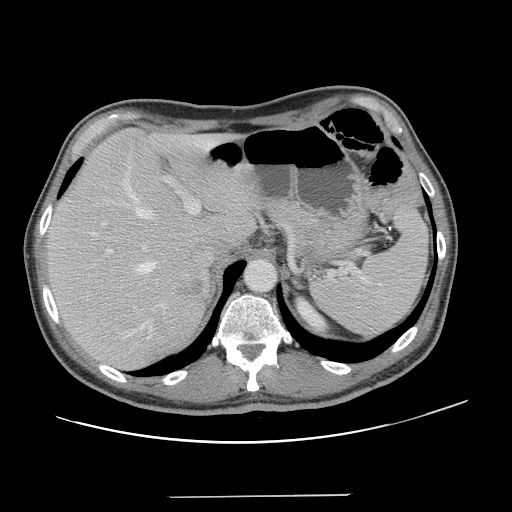
Contrast-enhanced abdominal CT, one axial slice; position 95 of 131 along the scan axis; 120 kVp; intravenous contrast given; soft-tissue window (W 400 / L 40 HU); 2.5 mm slice thickness; 512 × 512 image matrix. Male patient, age 60 years. From the clinical record (not read from this slice): diagnosis: colorectal cancer liver metastases, imaged before liver resection; multiple liver metastases: no; largest metastasis: 2.5 cm; disease in both lobes: no.
Structures marked on this image (outlined manually by an expert reader):
- hepatic veins: box from (x=94, y=179) to (x=157, y=331) px
- liver: (x=47, y=130)–(x=253, y=370)
- planned liver remnant (the part of the liver to remain after resection): (x=47, y=130)–(x=253, y=353)
- portal vein (with intrahepatic branches): (x=101, y=144)–(x=205, y=255)
- liver metastasis: (x=175, y=279)–(x=207, y=298)